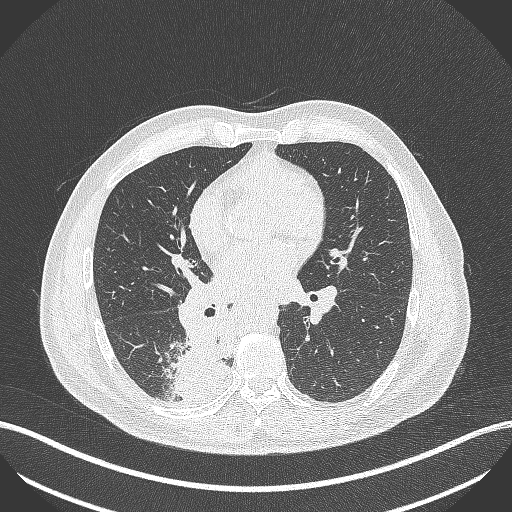
Chest CT, one axial slice. Slice 230 of 451 in the series (ordered by position). Reconstruction kernel B70f. 100 kVp. Lung window (W 1500 / L -600 HU). 1 mm slice thickness. 512 × 512 image matrix. Male patient, age 61 years. Case-level facts recorded for this patient, not image findings: clinical TNM (as recorded): T1 N0 M0.
Outlined on this slice (bounding box drawn by a radiologist):
- lung tumour (recorded histology: small cell carcinoma): bounding box (x1, y1, x2, y2) in pixels: (172, 316, 236, 410)